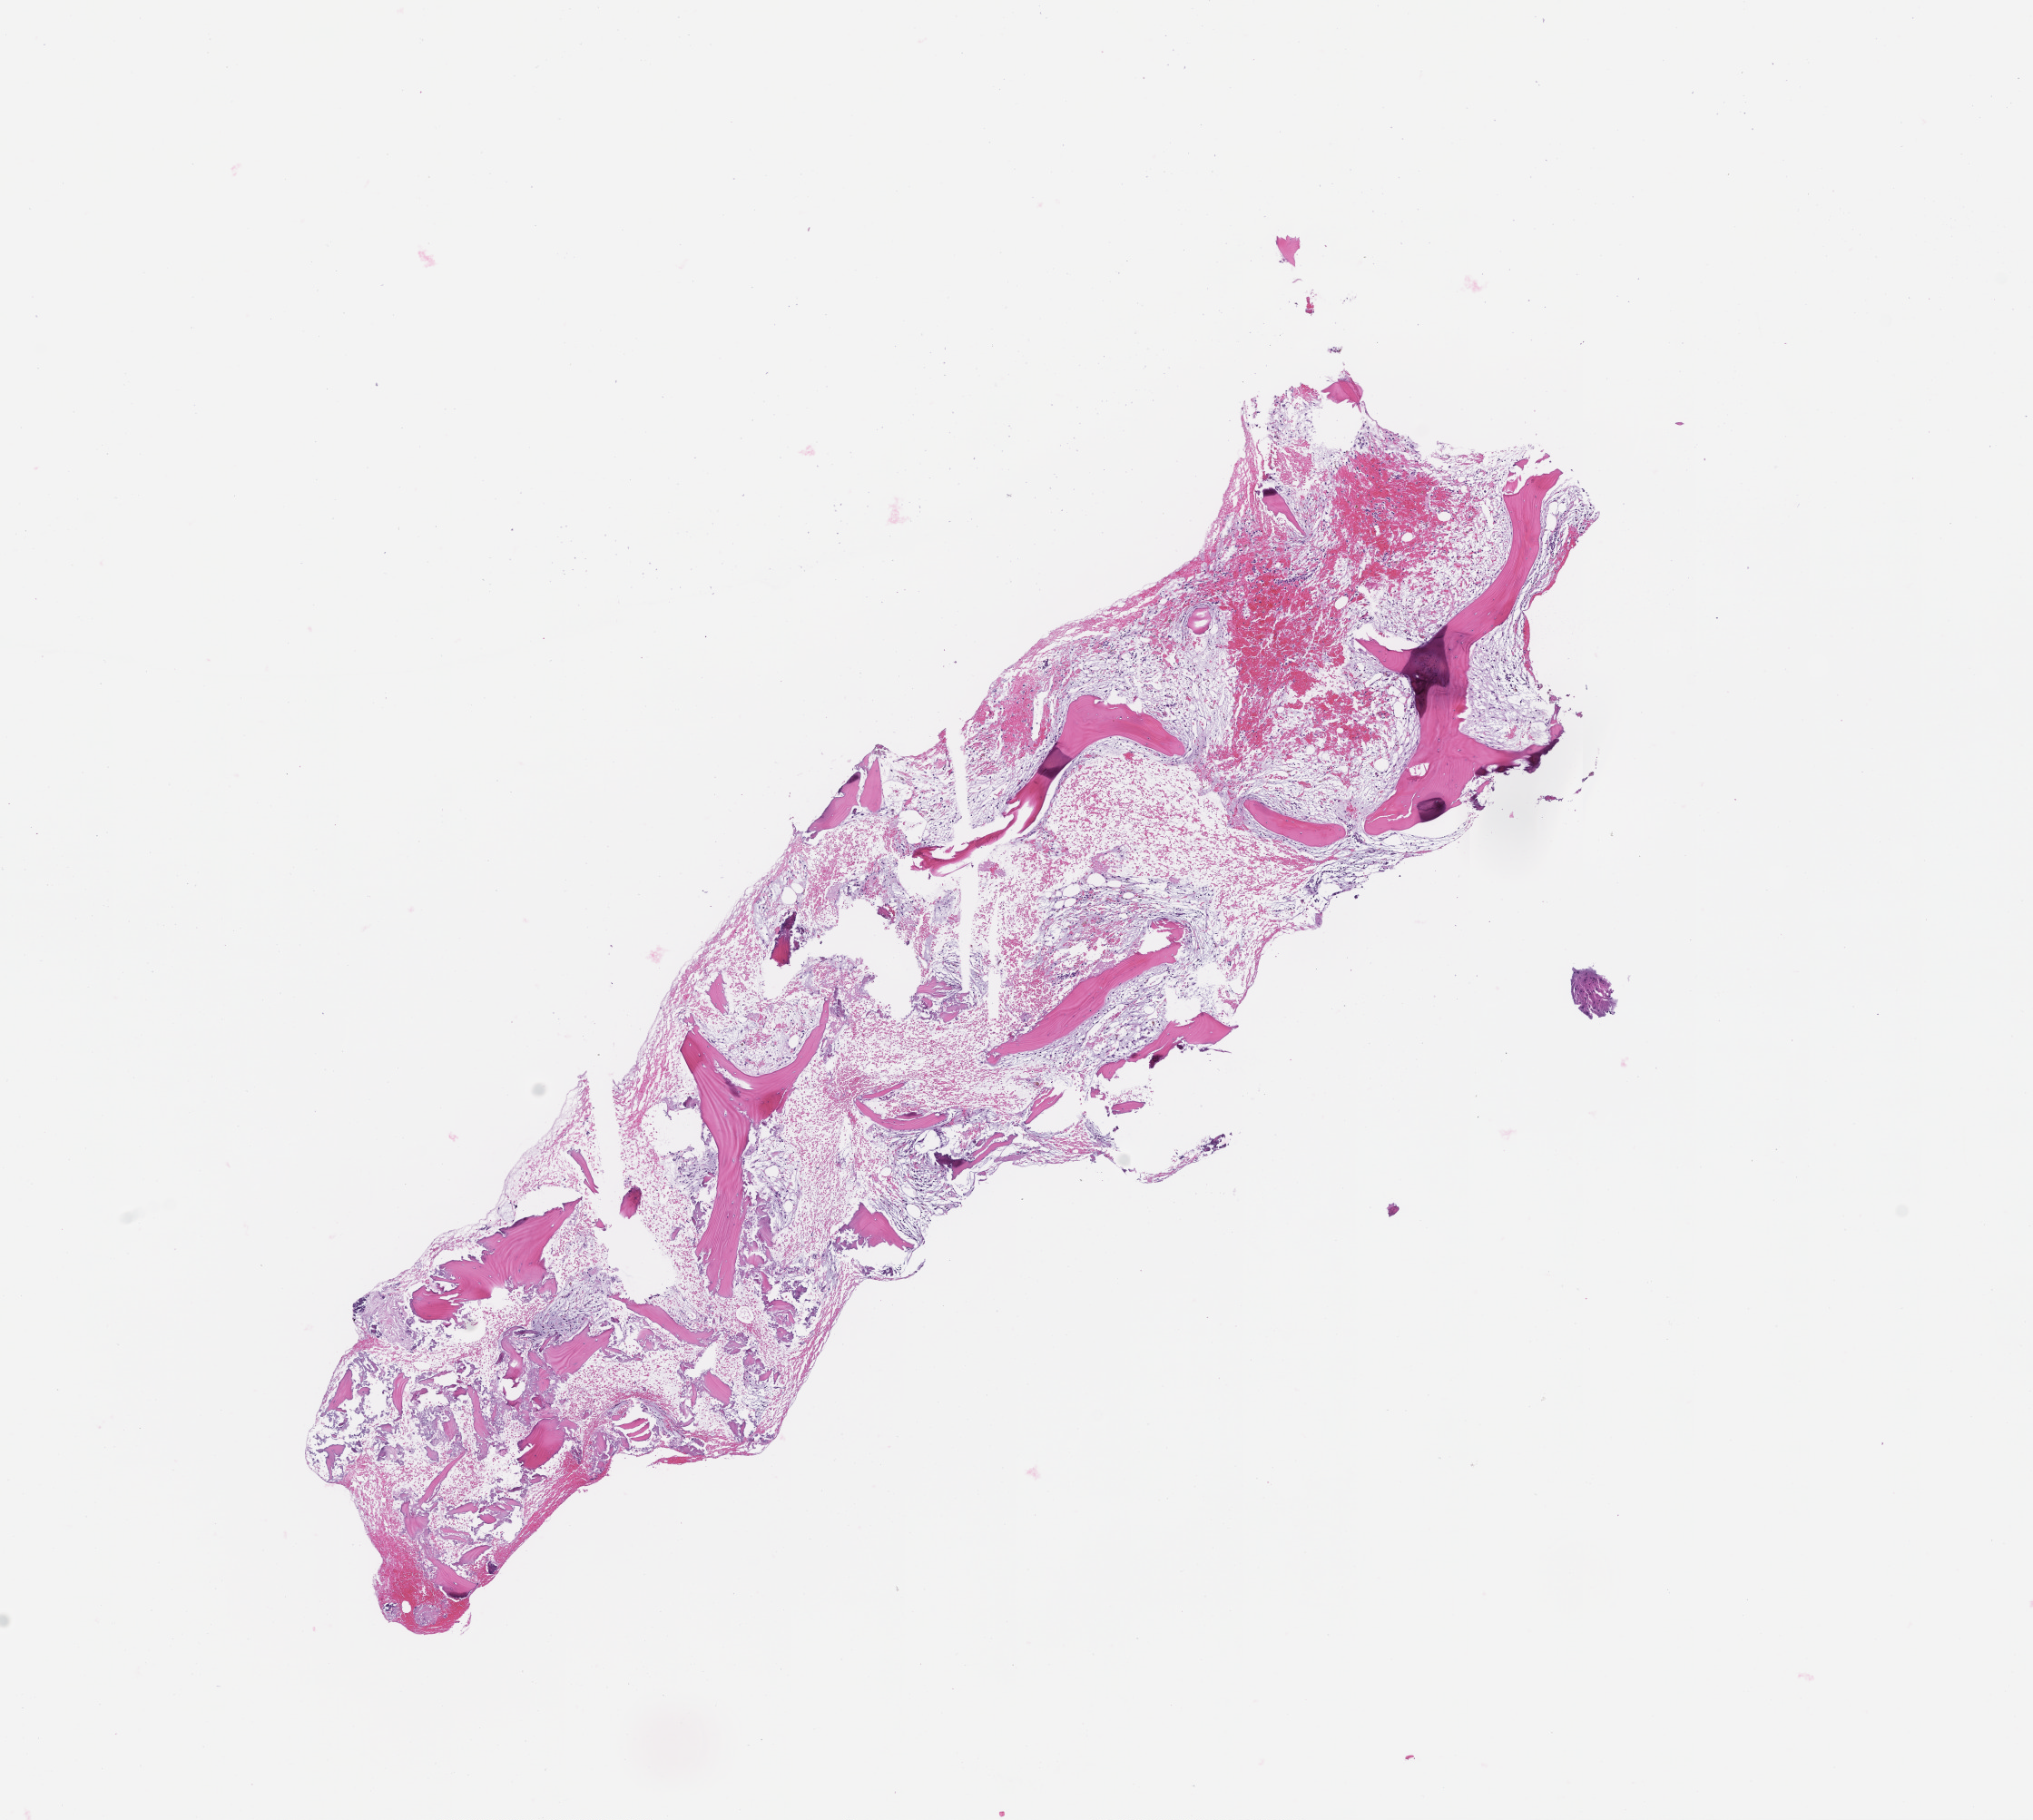
Haematoxylin and eosin whole-slide image — low-resolution overview of the scanned area, about 9.0 x 8.1 mm; FFPE section; site: bone marrow. Patient sex: female.
* this section: primary tumor
* diagnosis: Acute Myeloid Leukemia Not Otherwise Specified